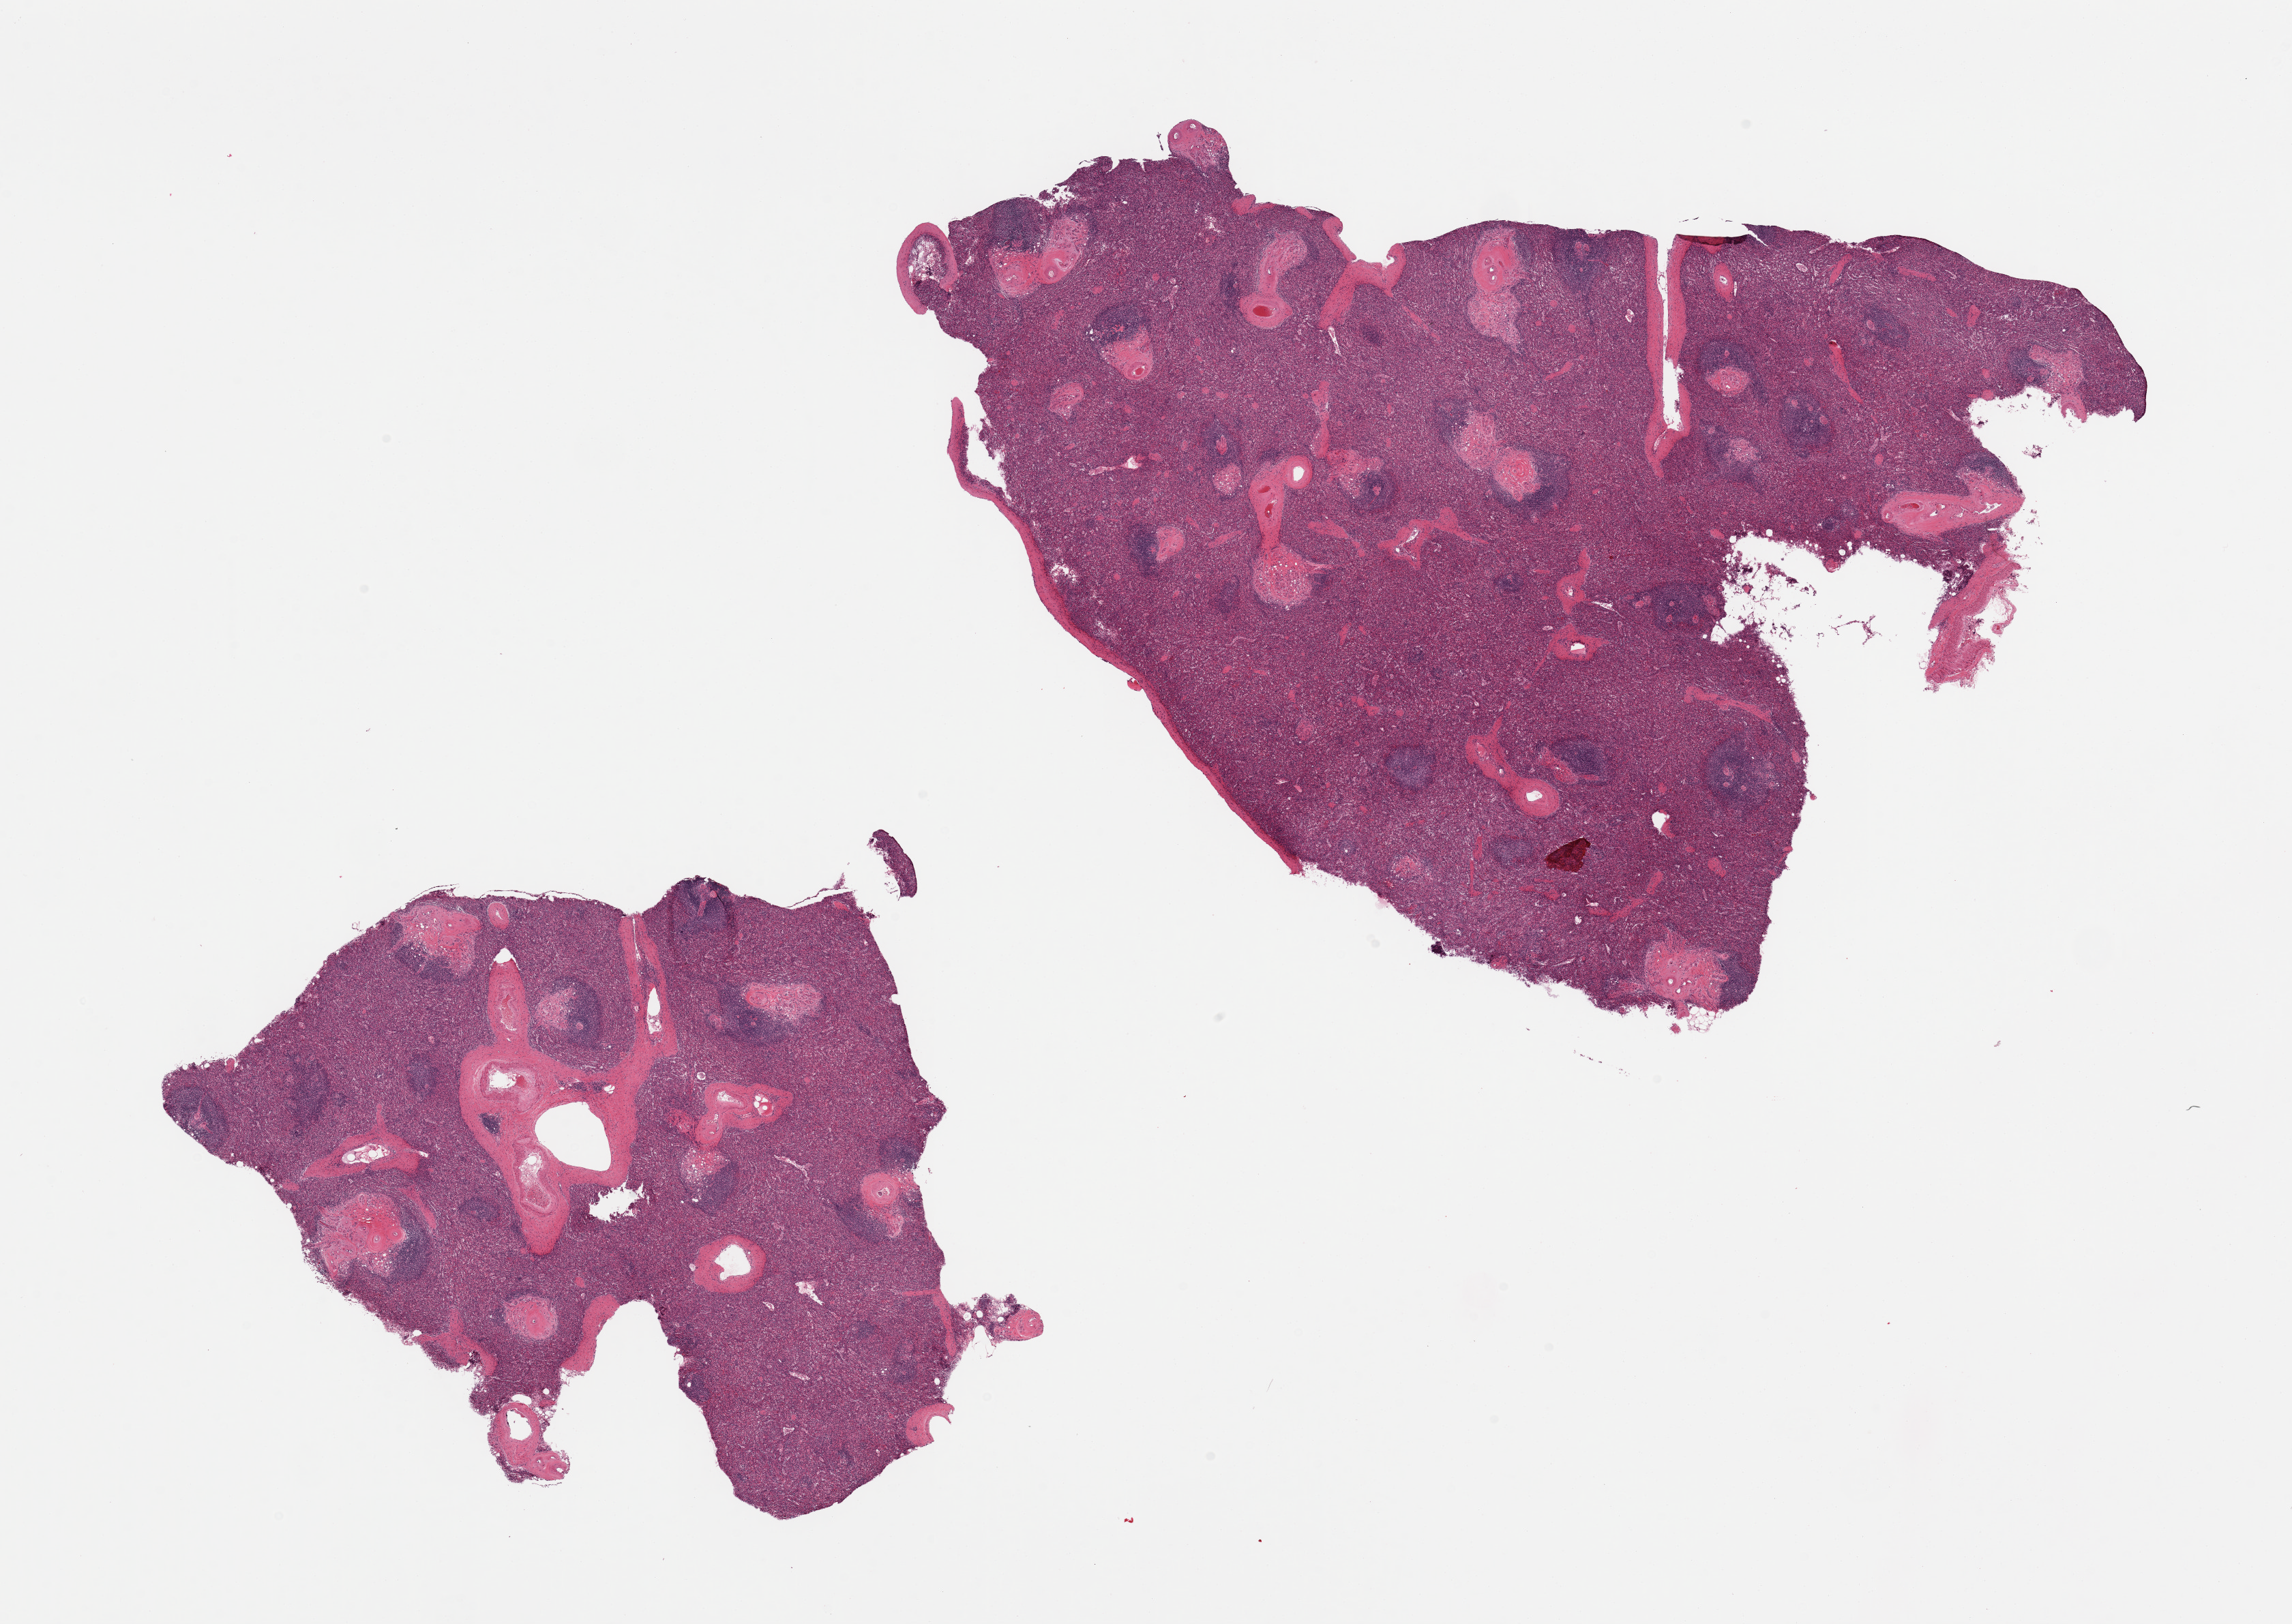
Hematoxylin and eosin (H&E) whole-slide image — shown as a low-resolution overview of the whole scanned area (about 26.6 x 18.8 mm), PAXgene-fixed paraffin-embedded (PFPE) section, section of spleen (target tissue), tissue donor sample. Female donor.
Pathologist's review note for this sample: 2 pieces, proliferation of small vascular channels (?hemangioma) and arterial thickening. Dr. Allen Burke and Dr. Sobin were consulted.